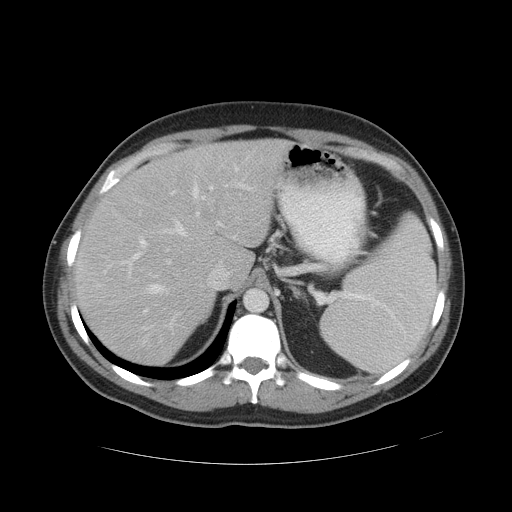
Contrast-enhanced abdominal CT, one axial slice; slice 36 of 49 in the series (ordered by position); reconstruction kernel STANDARD; 120 kVp; intravenous contrast given; soft-tissue window (W 400 / L 40 HU); 5 mm slice thickness; 512 × 512 image matrix, field of view 422 × 422 mm. Male patient, age 42 years. Case-level facts recorded for this patient, not image findings: diagnosis: colorectal cancer liver metastases, imaged before liver resection; multiple liver metastases: yes; largest metastasis: 2.8 cm.
Structures marked on this image (expert manual segmentation):
- hepatic veins: bounding box (x1, y1, x2, y2) in pixels: (145, 166, 253, 329)
- liver: (76, 141, 283, 366)
- planned liver remnant (the part of the liver to remain after resection): (76, 141, 284, 366)
- portal vein (with intrahepatic branches): (121, 183, 255, 312)